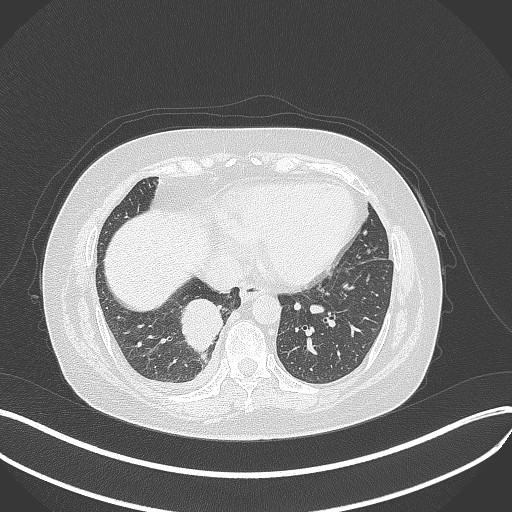
Chest CT, one axial slice; 120 kVp; lung window (W 1500 / L -600 HU); 512 × 512 image matrix, field of view 400 × 400 mm. Female patient, age 56 years. From the clinical record (not read from this slice): clinical TNM (as recorded): T2b N1 M0.
Structures marked on this image (rectangle marked by the reading radiologist):
- lung tumour (recorded histology: small cell carcinoma): bounding box [x1, y1, x2, y2] px = [179, 294, 225, 359]